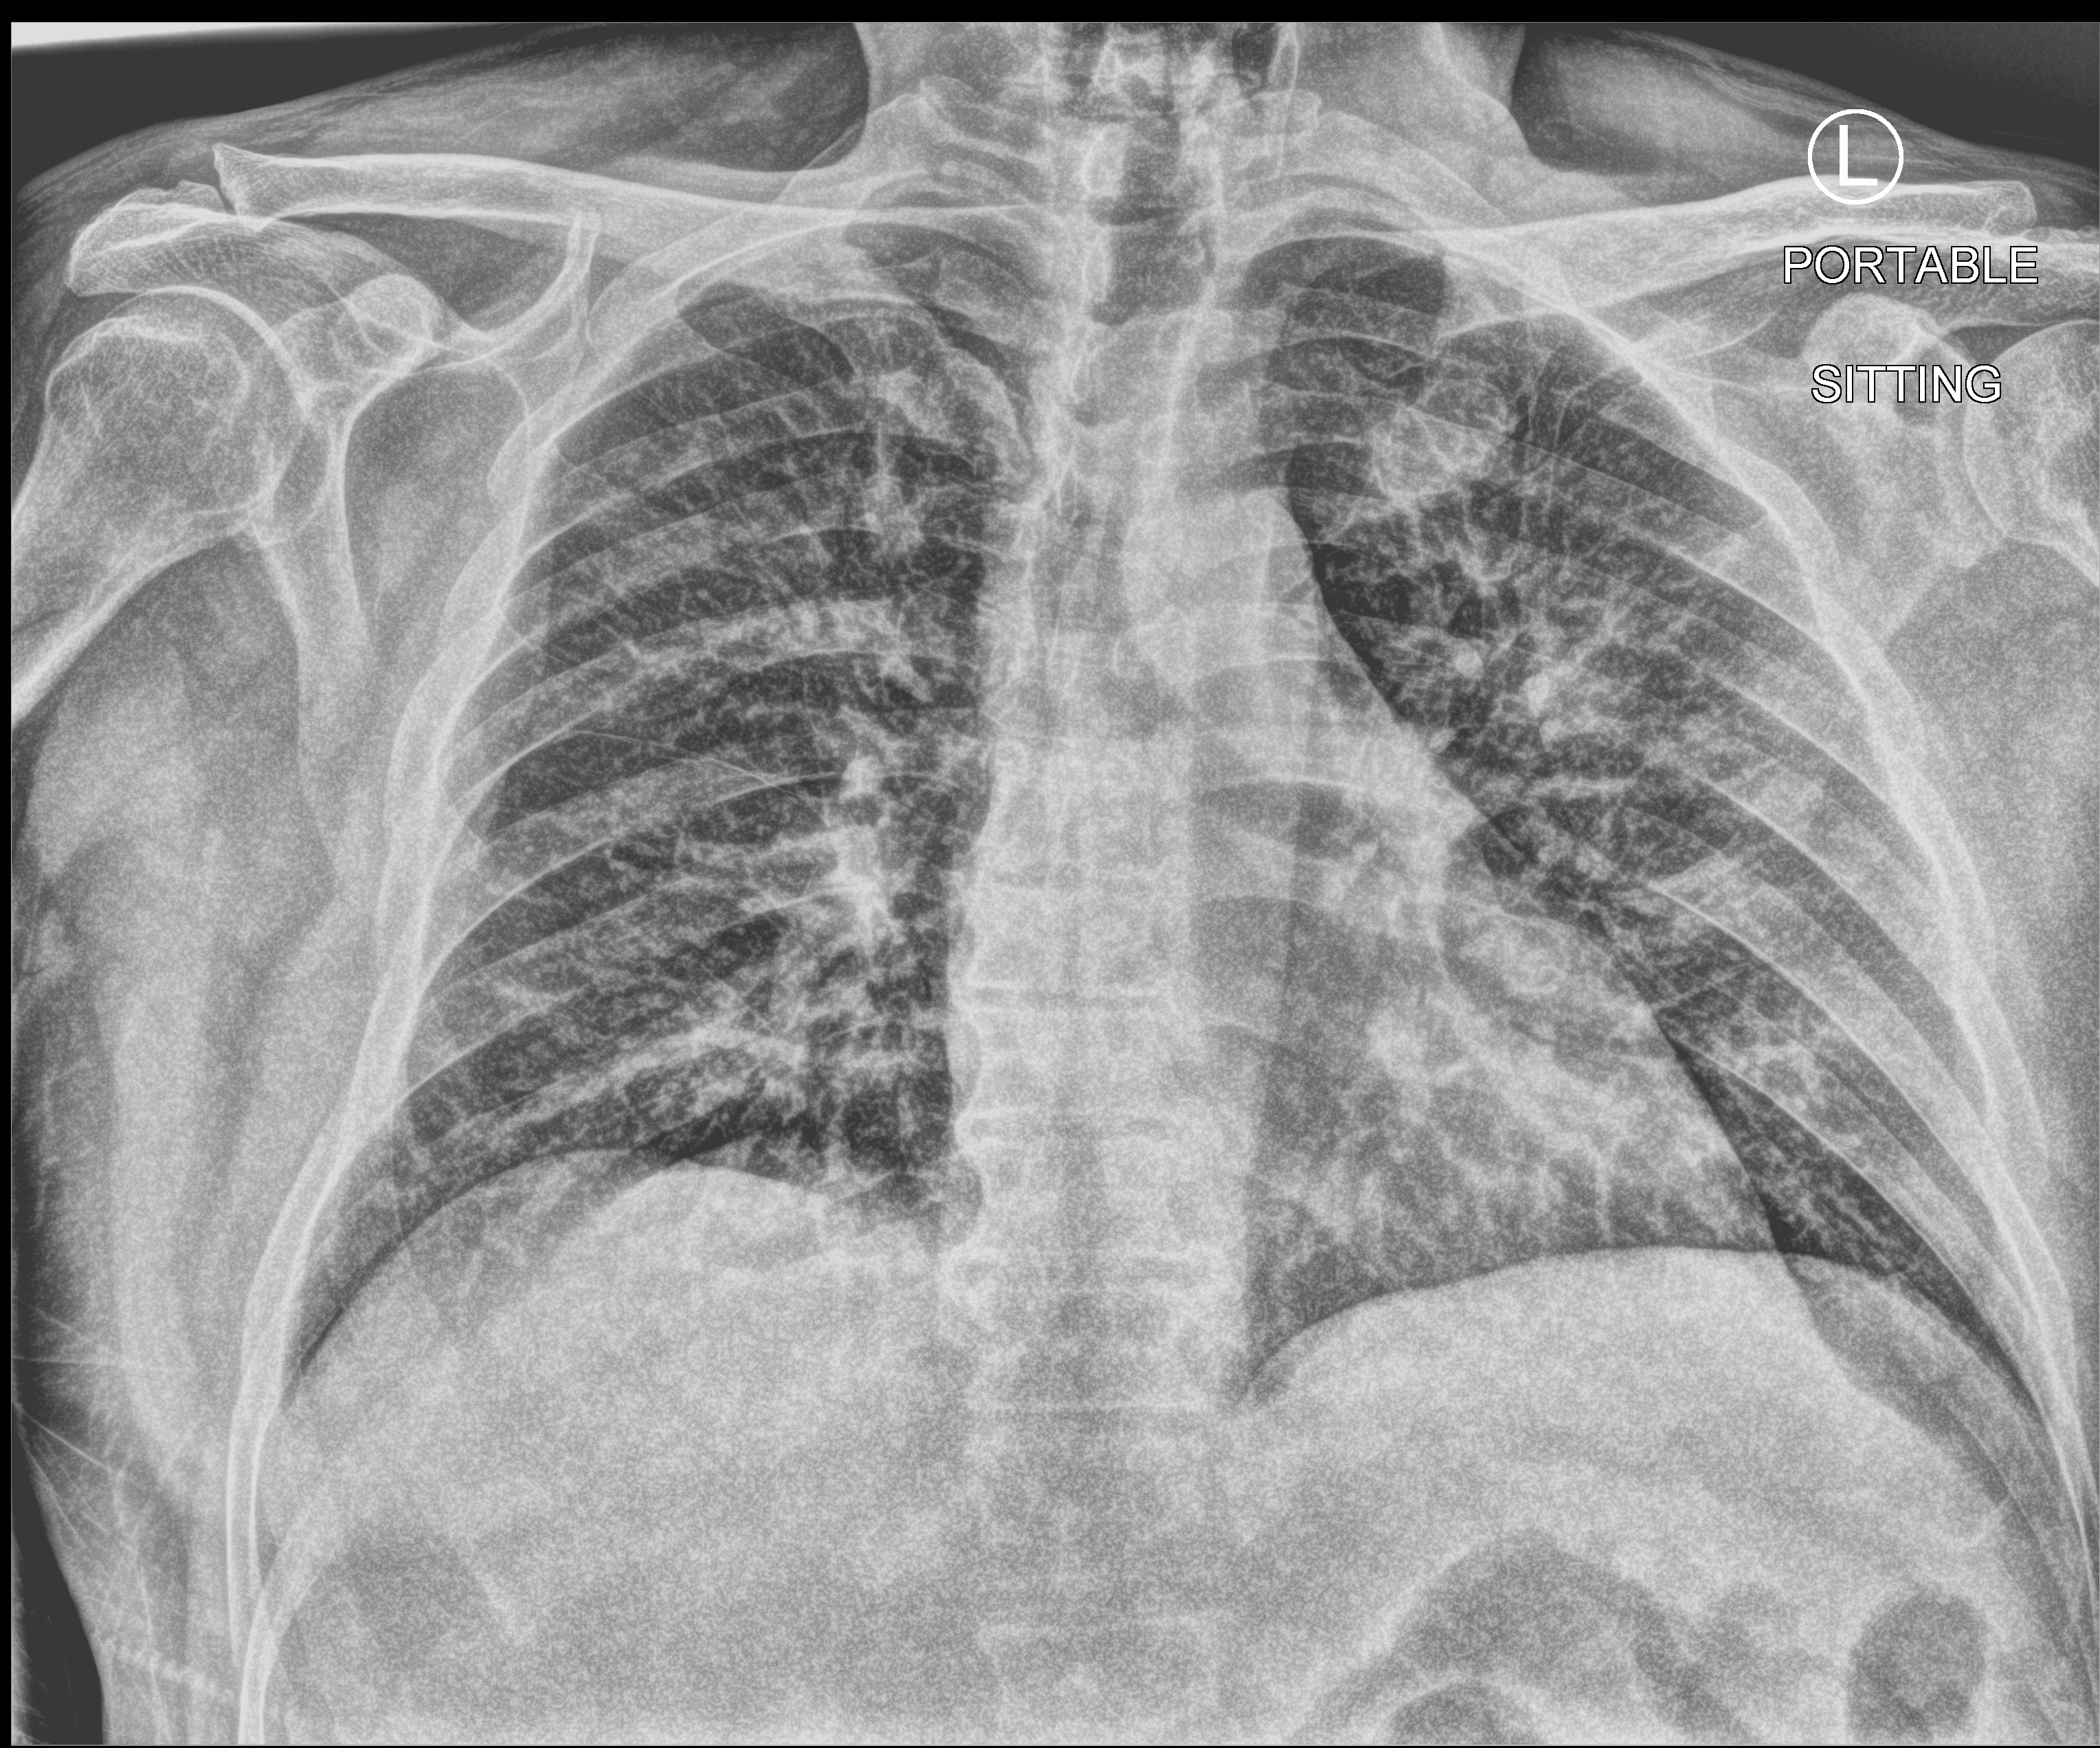
Portable chest radiograph. Patient hospitalised with COVID-19; male, aged 18–59 years.
Hospital-stay facts (about this admission, not read from this image; timing relative to this image not recorded):
- diabetes (admission record): no
- mechanically ventilated during this hospital stay: no
- COPD (admission record): no